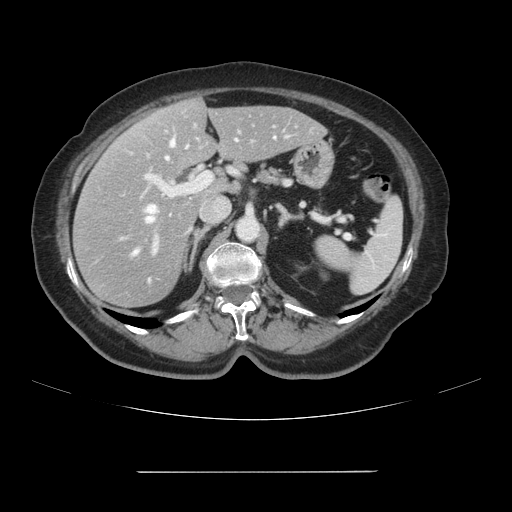
Contrast-enhanced abdominal CT, one axial slice. Position 58 of 111 along the scan axis. 120 kVp. Soft-tissue window (W 400 / L 40 HU). 2.5 mm slice thickness. 512 × 512 image matrix, field of view 400 × 400 mm. Female patient, age 74 years. Case-level facts recorded for this patient, not image findings: diagnosis: colorectal cancer liver metastases, imaged before liver resection; multiple liver metastases: yes; largest metastasis: 1.1 cm.
Outlined on this slice (manually delineated by an expert):
- hepatic veins: bounding box [x1, y1, x2, y2] px = [134, 137, 275, 254]
- liver: [75, 100, 324, 307]
- planned liver remnant (the part of the liver to remain after resection): [146, 100, 324, 195]
- portal vein (with intrahepatic branches): [122, 124, 298, 253]